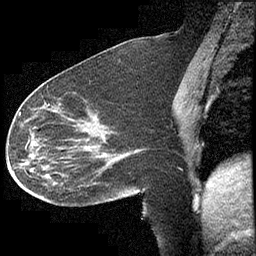
Breast MRI (dynamic contrast-enhanced), one sagittal slice. Position 169 of 232 along the scan axis. Dynamic contrast-enhanced study with each time point stored as its own series, time point 2 of 4 at this slice position (early post-contrast, ordered by acquisition time). 1.5 T. TE 4.2 ms, TR 6.7 ms. 3 mm slice thickness. 256 × 256 image matrix, field of view 200 × 200 mm. Female patient, age 63 years. Case-level facts recorded for this patient, not image findings: setting: breast cancer imaged before/during neoadjuvant chemotherapy; receptor status: triple-negative.
Outlined on this slice (semi-automatically segmented with operator editing):
- analysis volume of interest (the breast-tissue region the enhancement analysis was run in; not a lesion): bounding box <13,90,140,207> (left, top, right, bottom; pixels)
- tumour enhancement mask (voxels above the 70 % enhancement threshold inside the analysis volume of interest): <19,112,125,155>